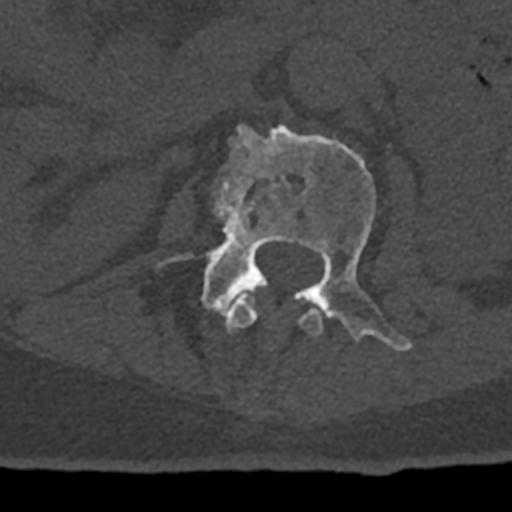
CT including the spine, one axial slice; position 391 of 797 along the scan axis; reconstruction kernel Br40s/3; 120 kVp; bone window (W 1800 / L 400 HU); 0.5 mm slice thickness; 512 × 512 image matrix, field of view 160 × 160 mm. Patient: male, 74 years. From the clinical record (not read from this slice): primary cancer: renal.
Outlined on this slice (semi-automatically segmented with operator editing):
- L1 vertebra: bounding box <225,289,323,336> (left, top, right, bottom; pixels)
- L2 vertebra: <160,124,412,351>